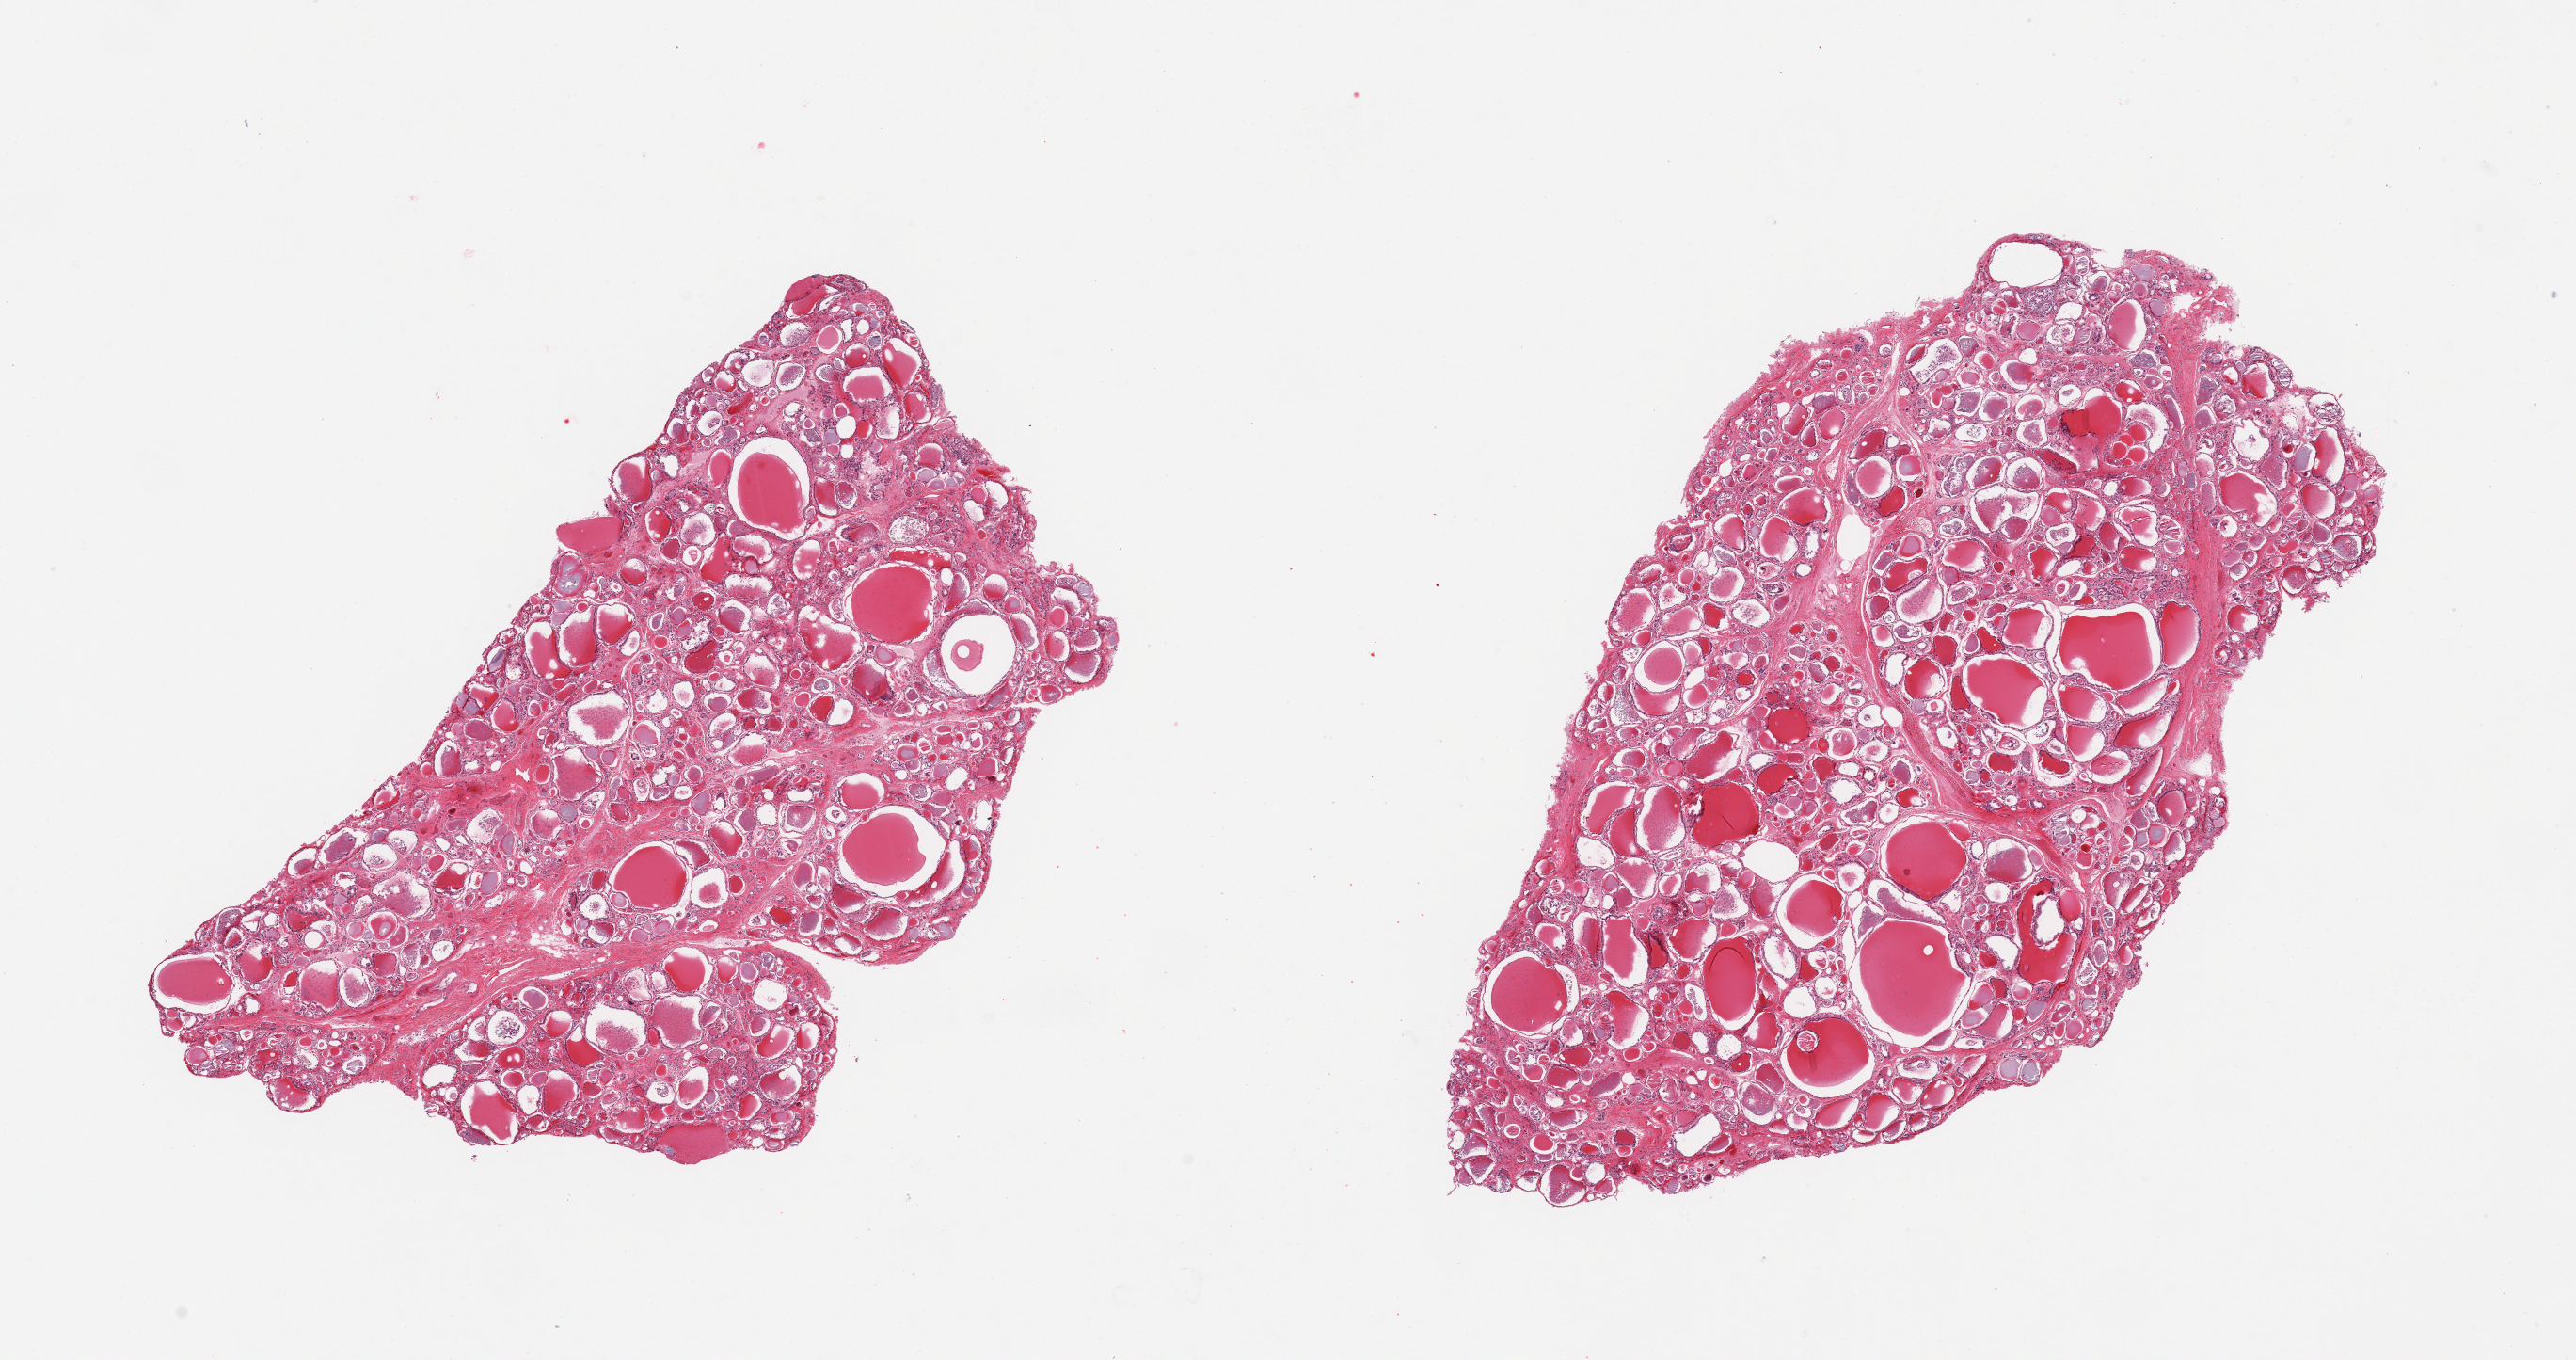
Digitized haematoxylin and eosin-stained section, a low-resolution overview of the entire scanned area, about 21.7 x 11.4 mm (acquisition: 20x scan); PAXgene-fixed paraffin-embedded (PFPE) section; section of thyroid (target tissue); donor tissue sample. Donor: male.
Review note (as recorded): 2 pieces; nodular hyperplasia with prominent amounts of colloid.